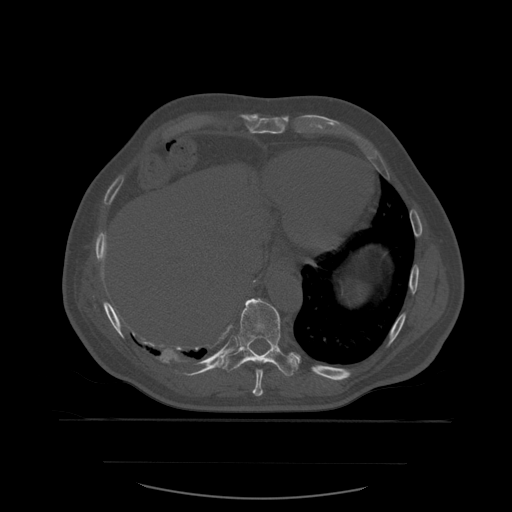
CT including the spine, one axial slice; position 323 of 590 along the scan axis; bone window (W 1800 / L 400 HU); 512 × 512 image matrix, field of view 479 × 479 mm. Patient age 71 years. Case-level facts recorded for this patient, not image findings: primary cancer: lung.
Structures marked on this image (semi-automatically segmented with operator editing):
- T10 vertebra: bounding box [x1, y1, x2, y2] px = [226, 298, 299, 377]
- T9 vertebra: [253, 370, 264, 397]